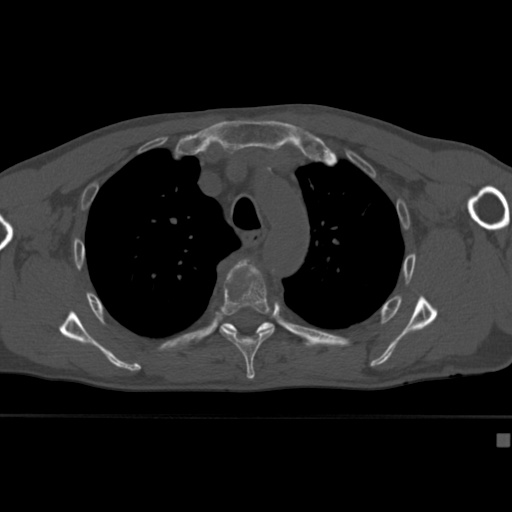
CT including the spine, one axial slice. Slice 307 of 430 in the series (ordered by position). Reconstruction kernel Br40s. 120 kVp. Bone window (W 1800 / L 400 HU). 1.5 mm slice thickness. 512 × 512 image matrix, field of view 337 × 337 mm. Patient: male, 64 years. From the clinical record (not read from this slice): primary cancer: uterus; vertebrae with lytic lesions (as recorded): T1, T4, T5, T7, L5.
Outlined on this slice (semi-automatic segmentation, software-assisted and operator-edited):
- T4 vertebra: bounding box <228,258,254,275> (left, top, right, bottom; pixels)
- T5 vertebra: <220,265,275,382>
- T6 vertebra: <223,322,291,348>